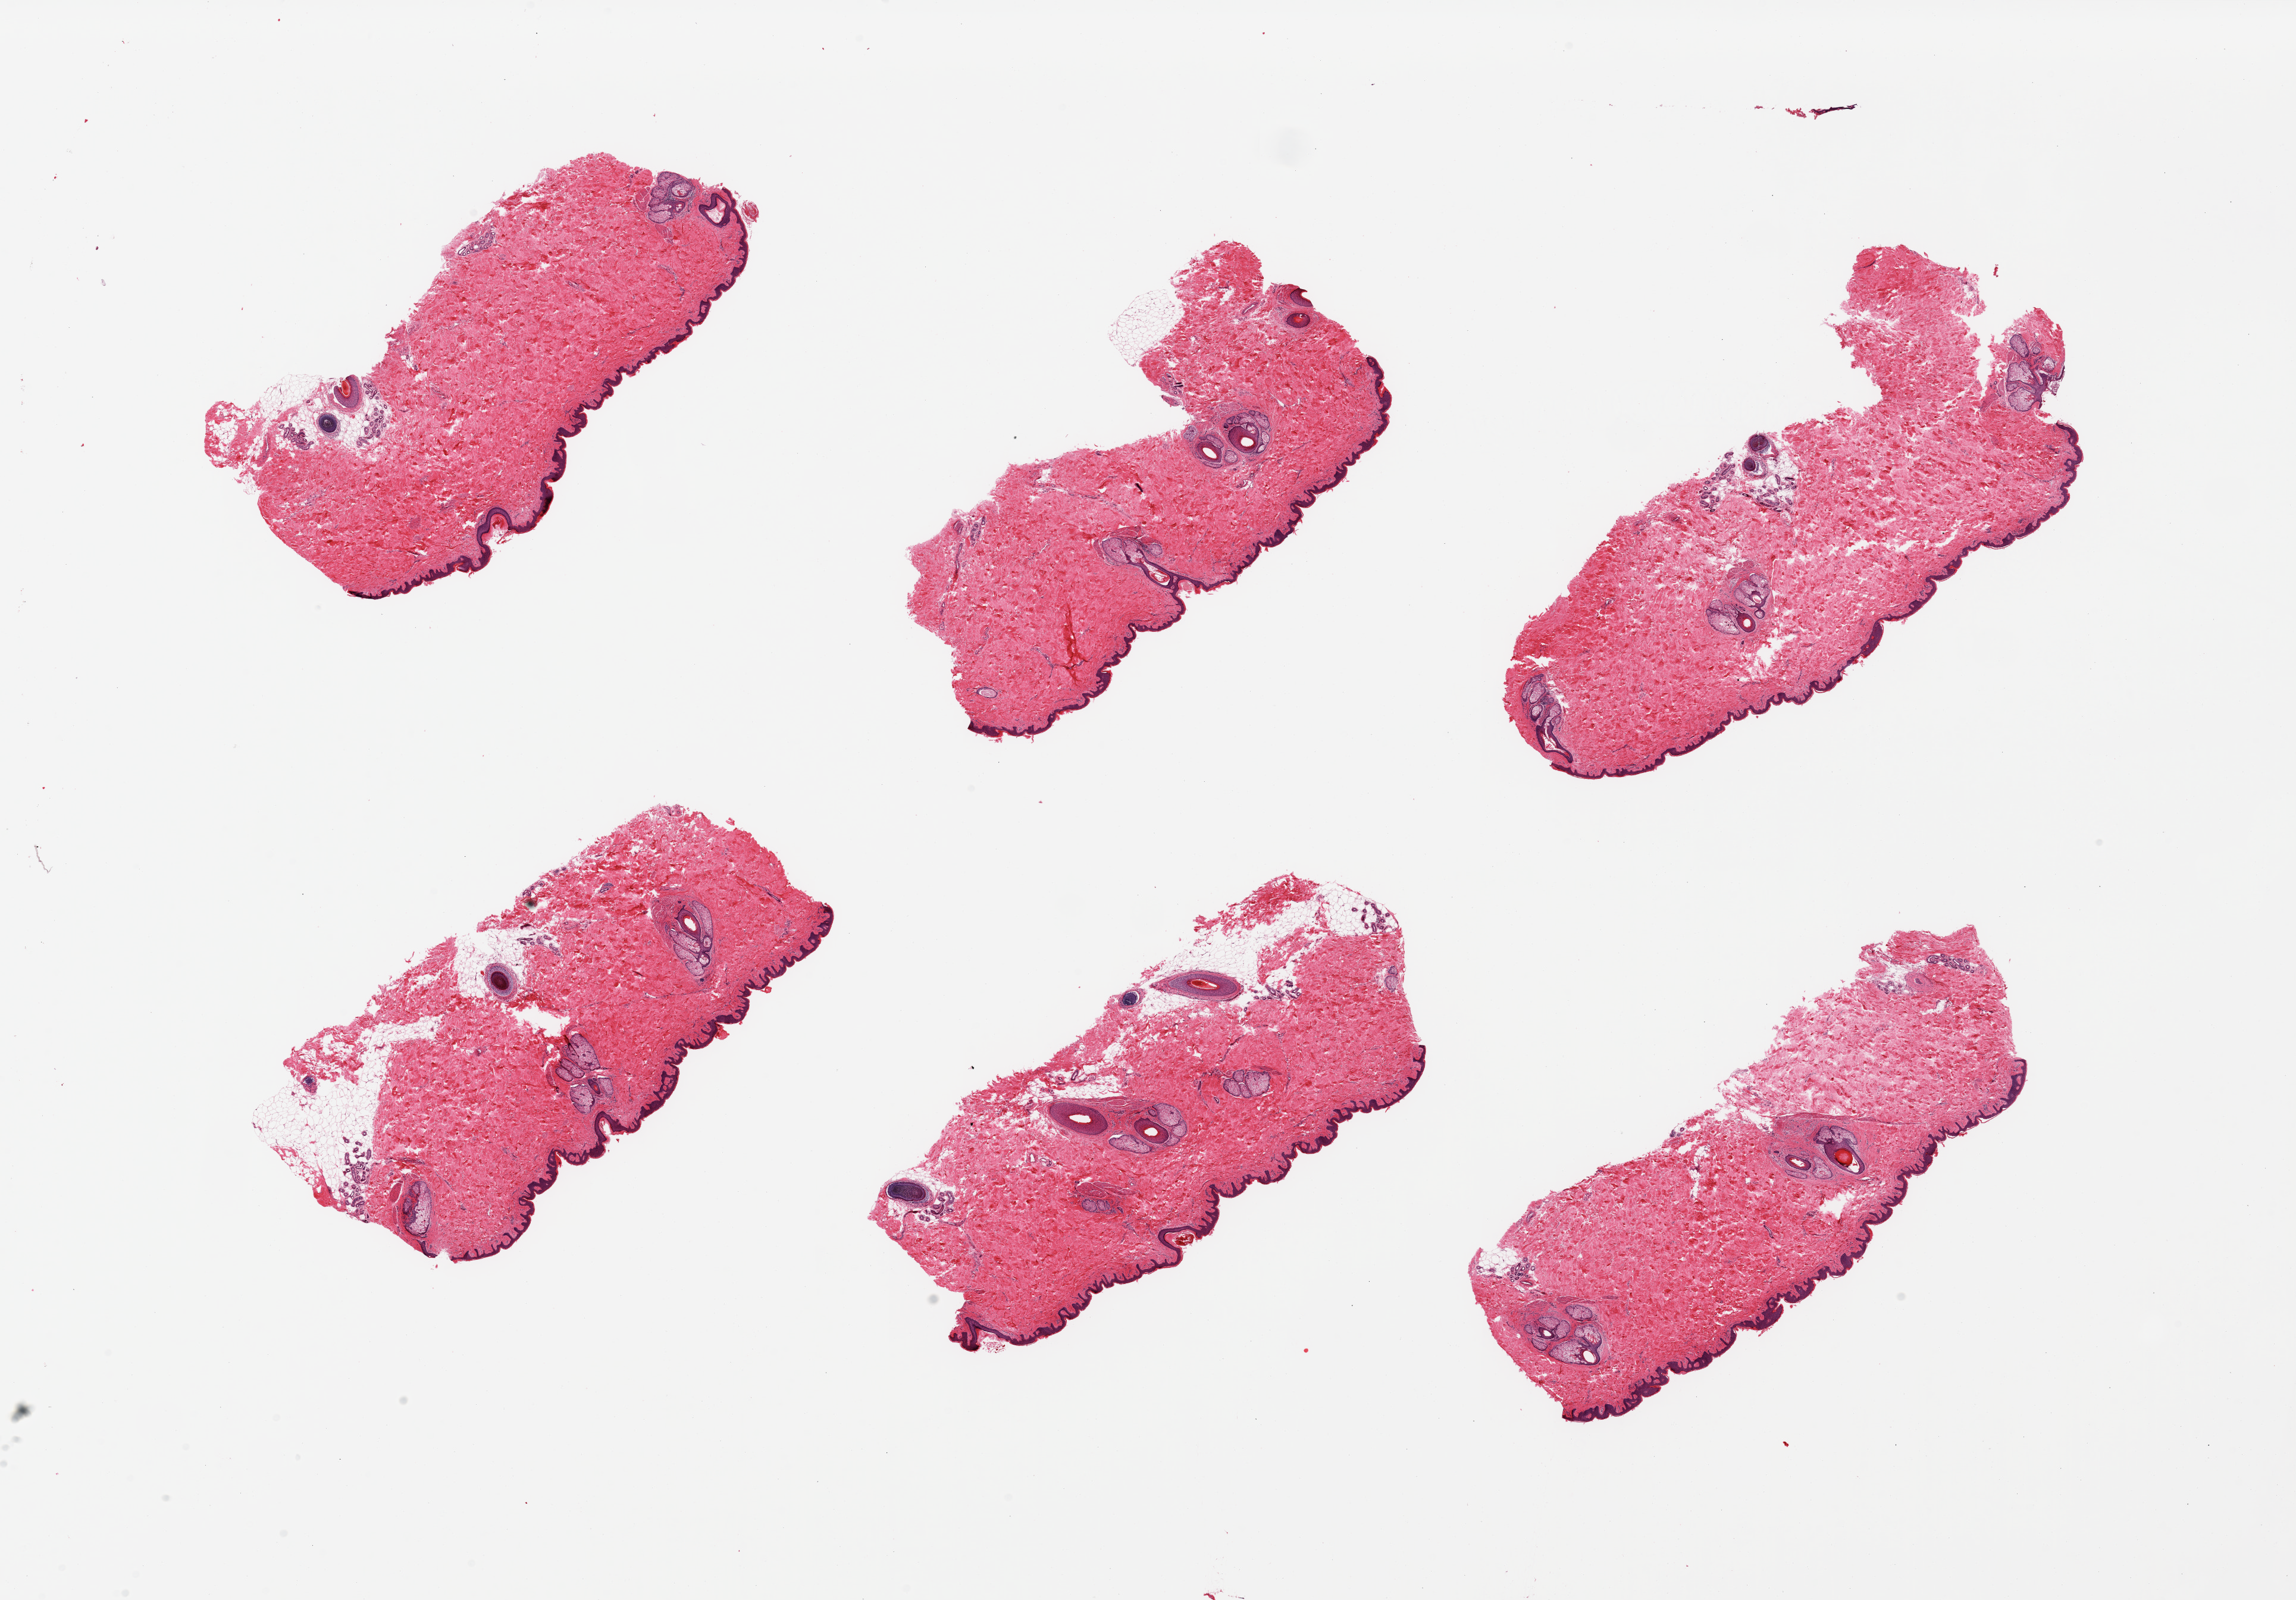
Whole-slide image, hematoxylin and eosin (H&E) stain, whole scanned area (about 30.5 x 21.3 mm) shown as a low-resolution overview. PAXgene-fixed paraffin-embedded (PFPE) section. Sampled site (target tissue): skin of suprapubic region. Tissue donor sample.
Pathologist's review note for this sample: 6 pieces, squamous epithelium is ~50 microns; trade dermal fat.